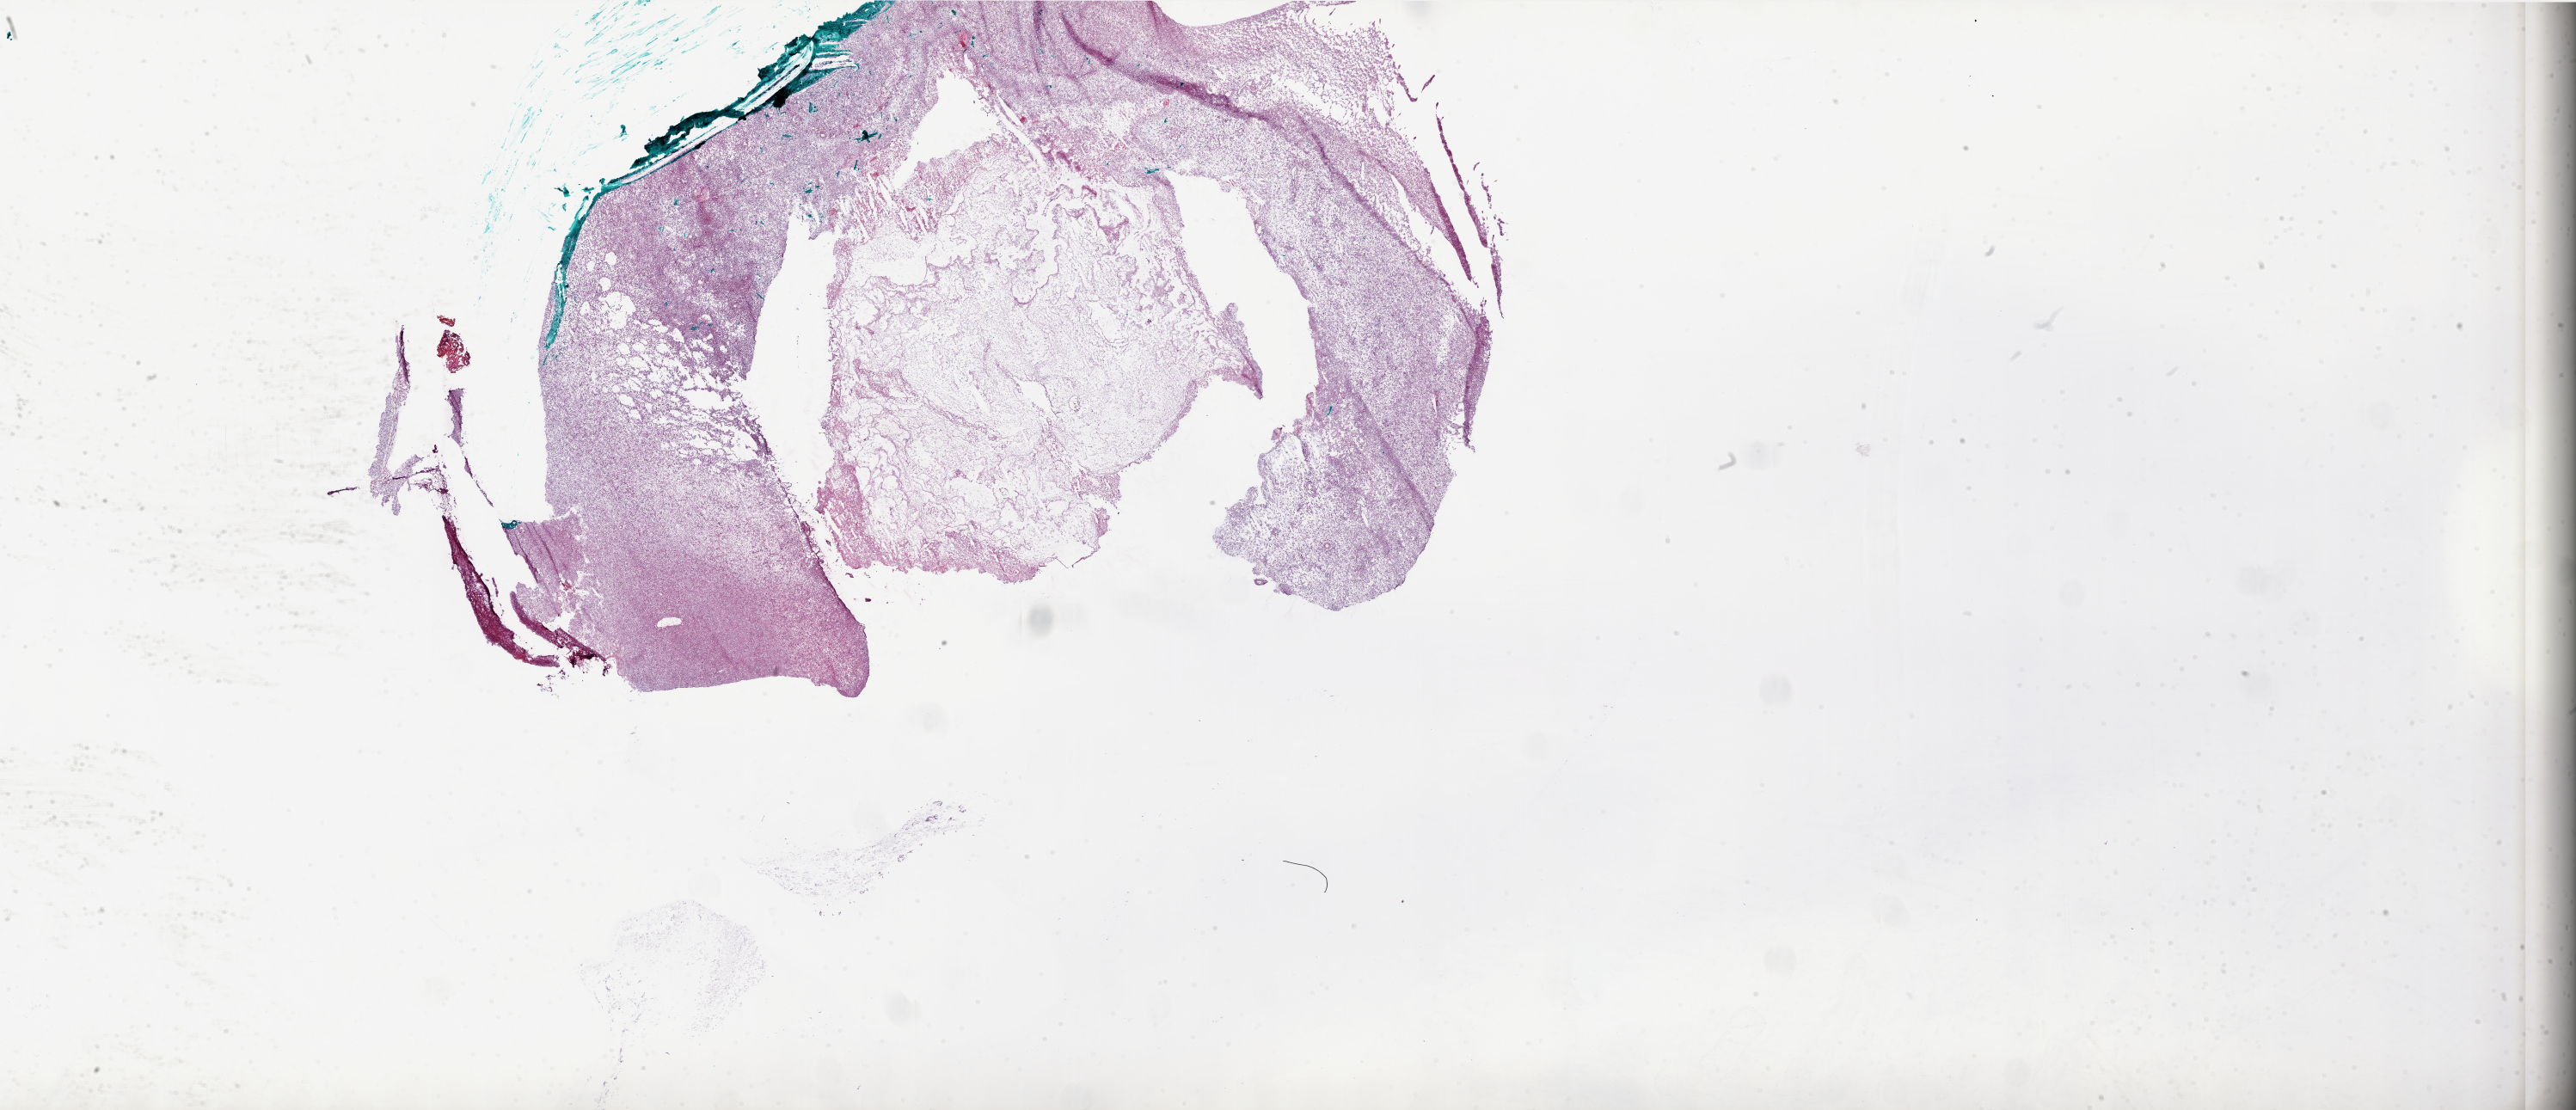
Digitized Hematoxylin and eosin (H&E) stained tissue section (whole slide), whole scanned area (about 48.0 x 20.7 mm, acquisition: 20x scan) shown as a low-resolution overview, frozen section from the bottom of the tissue portion, brain, primary tumour sample. Patient: male, age at initial diagnosis 61 years. Slide review estimates, as recorded: tumour cells 40%, tumour nuclei 80%, normal cells 10%, stromal cells 40%, necrosis 10%. Inflammatory infiltration, as recorded: lymphocyte infiltration 0%.
Histologic diagnosis: Glioblastoma.